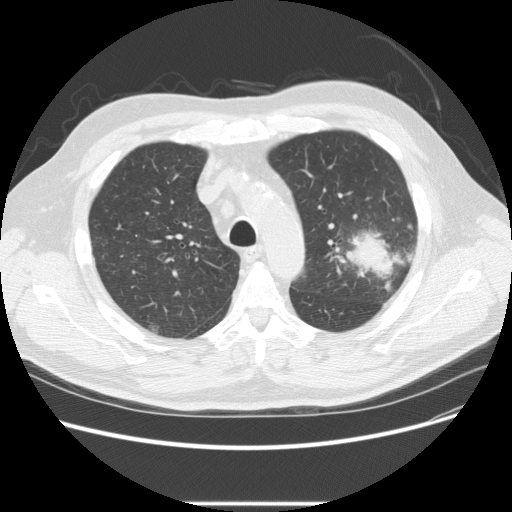
Chest CT (low-dose screening protocol), one axial image, first (baseline) screen, lung window (W 1500 / L -600 HU), 2.5 mm slice thickness, slice 65 of 233 in the series, 512 × 512 image matrix. Male participant, aged 73 years at enrolment. Former smoker at enrolment.
Expert reader's lesion annotation, bounding box <332,215,418,287> (left, top, right, bottom; pixels). The screening reader recorded 2 non-calcified nodules or masses ≥4 mm on this exam (left upper lobe, right upper lobe); which of them this box marks is not recorded. Official screen result: positive, change unspecified: nodule(s) >= 4 mm or enlarging nodule(s), mass(es), or other non-specific abnormalities suspicious for lung cancer. Later outcome: lung cancer diagnosed 11 days after this screen — bronchiolo-alveolar adenocarcinoma, NOS, other location, well differentiated (G1), stage IV (AJCC 6th edition).